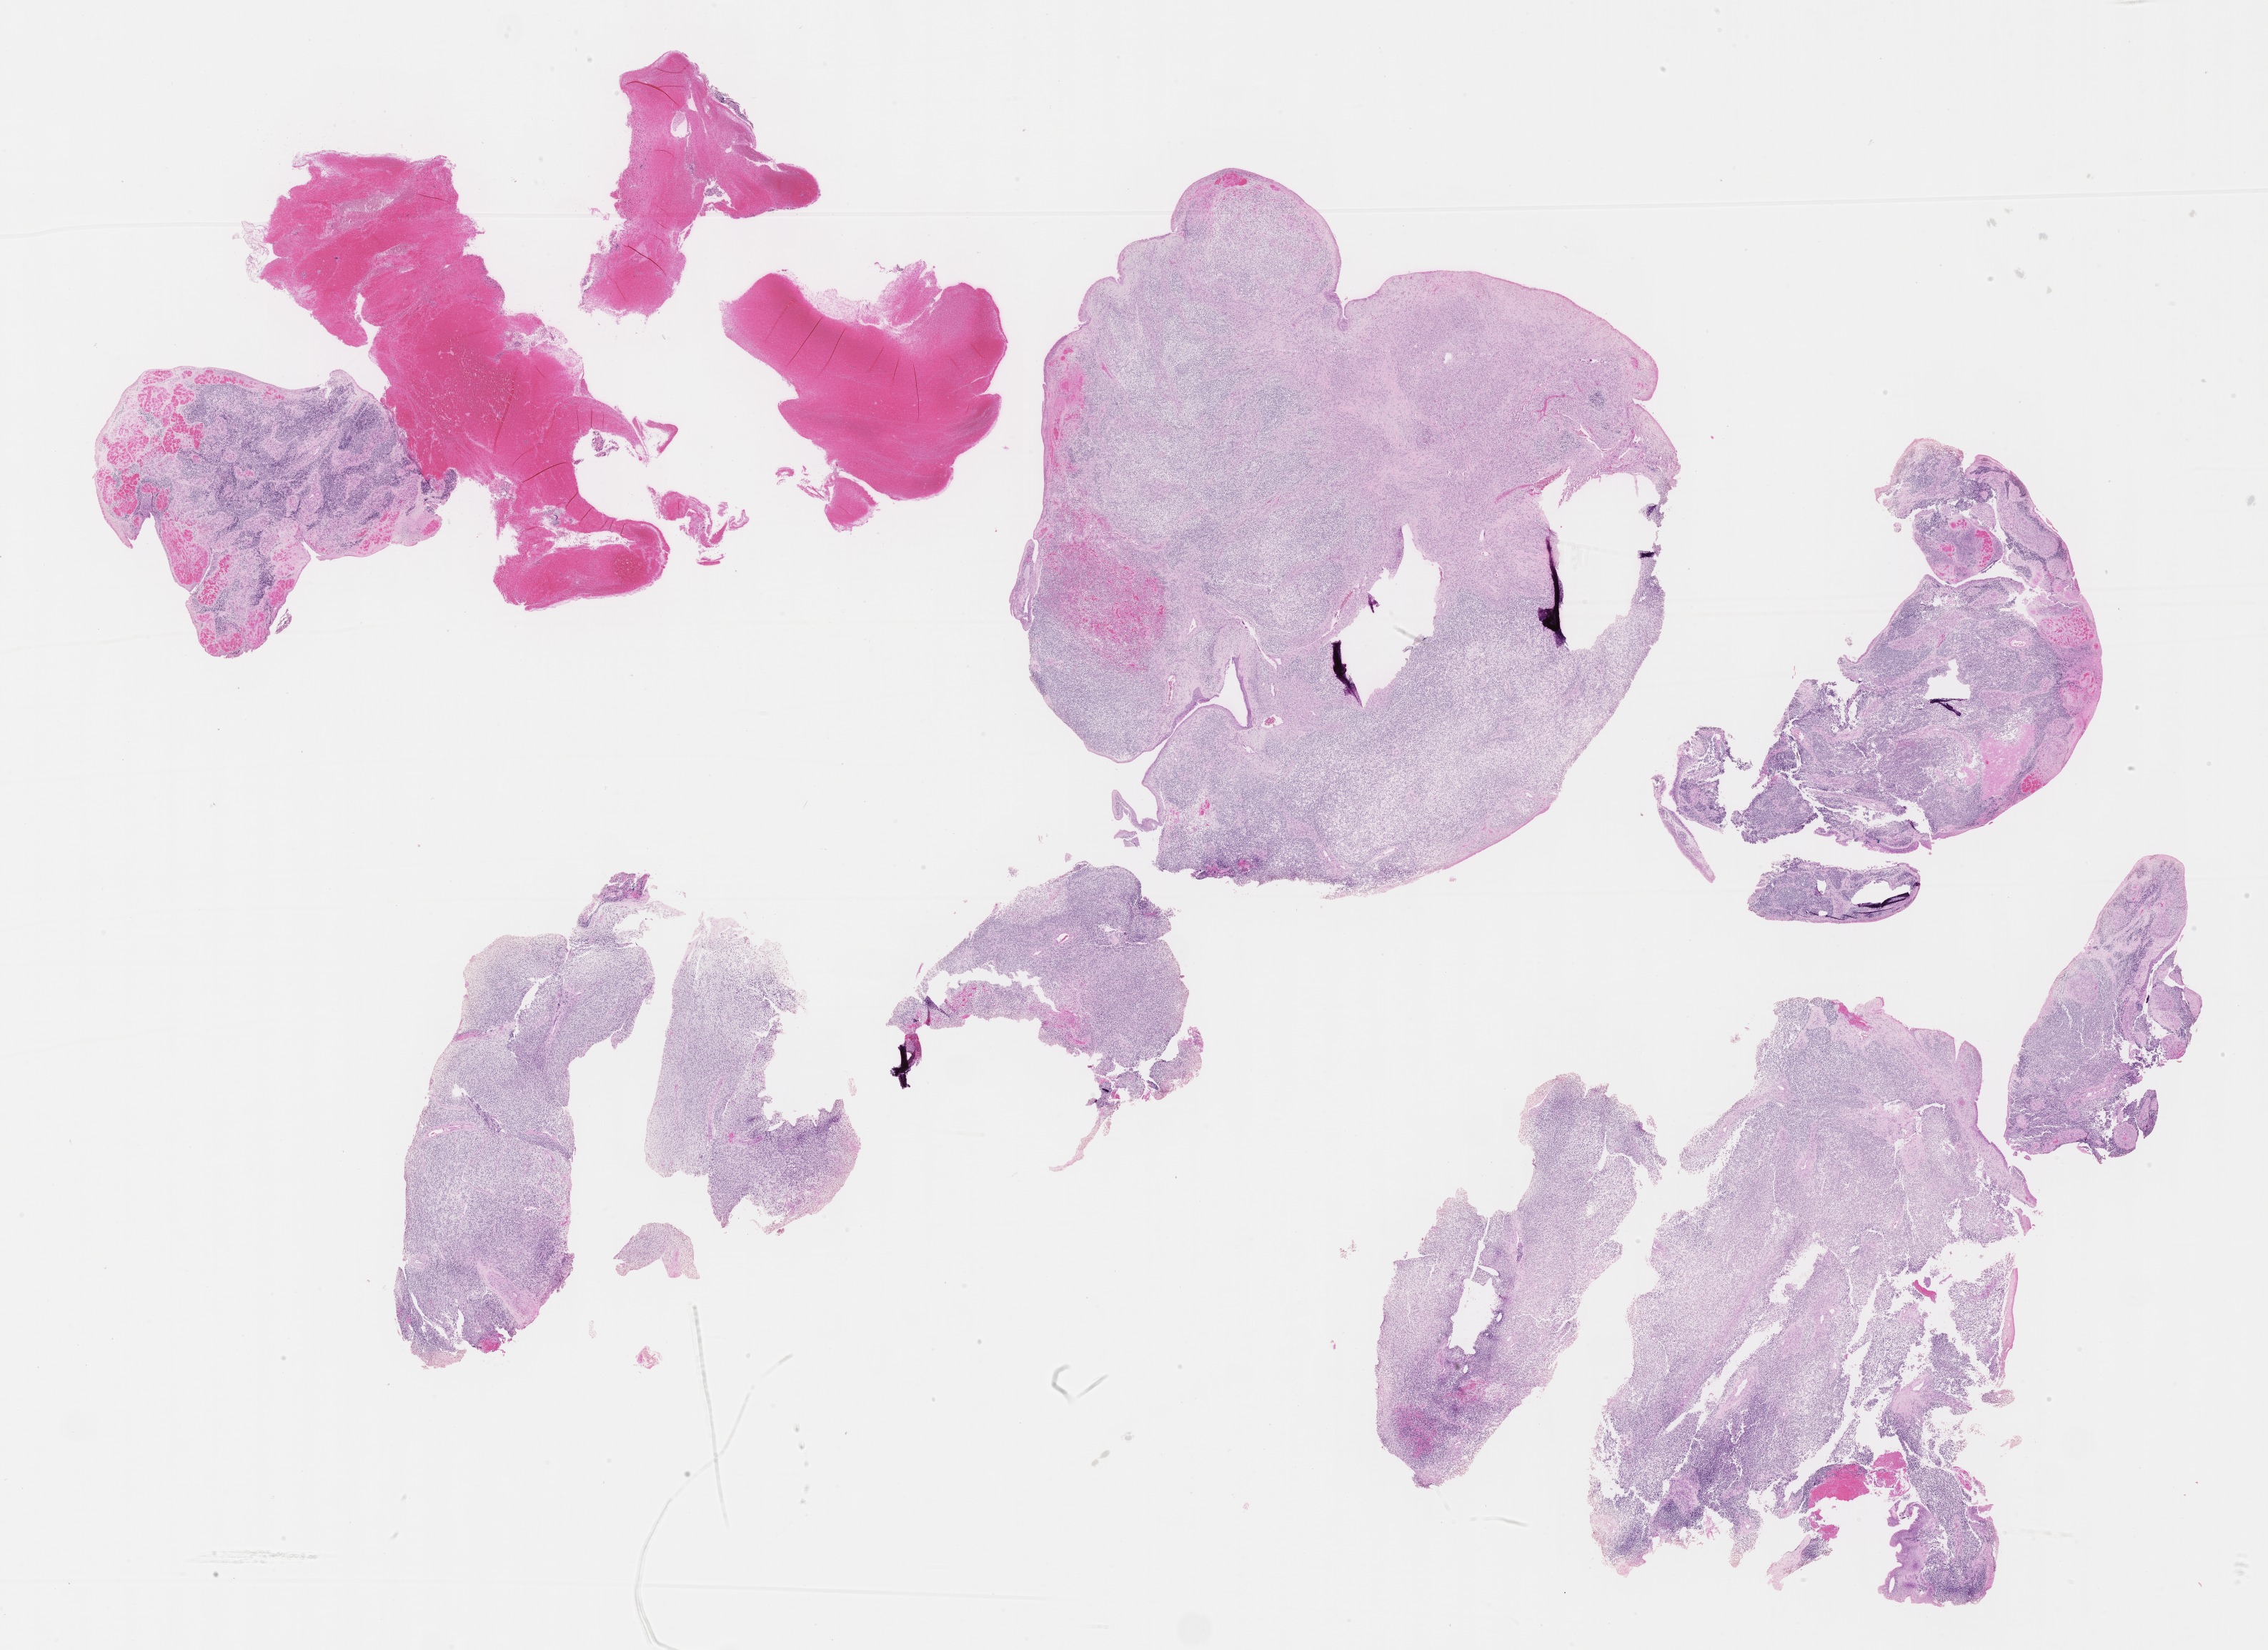
Digitized H&E-stained section of tumor tissue, whole scanned area (about 25.7 x 18.7 mm) shown as a low-resolution overview; FFPE section. Female patient, age at diagnosis 8.4 years.
- stage (as recorded): 3
- diagnosis: rhabdomyosarcoma; histological classification: embryonal rhabdomyosarcoma